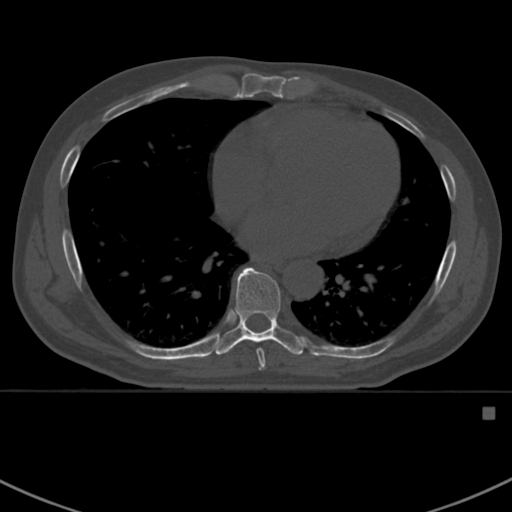
CT including the spine, one axial slice. Position 403 of 412 along the scan axis. Bone window (W 1800 / L 400 HU). 1.5 mm slice thickness. 512 × 512 image matrix, field of view 358 × 358 mm. Patient: male, 59 years. From the clinical record (not read from this slice): primary cancer: prostate.
Structures marked on this image (semi-automatic segmentation, software-assisted and operator-edited):
- T7 vertebra: bounding box <256,348,266,371> (left, top, right, bottom; pixels)
- T8 vertebra: <214,267,305,355>